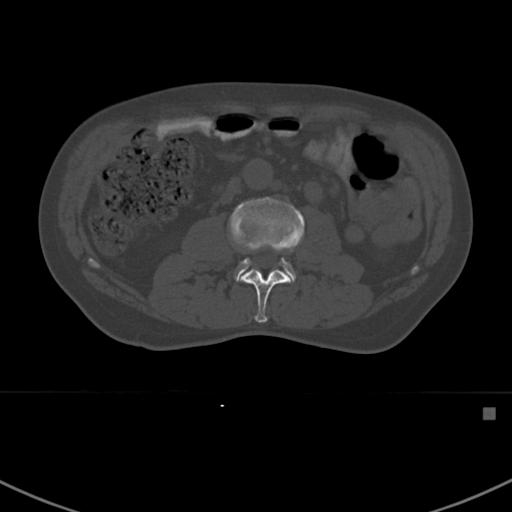
CT including the spine, one axial slice. Position 276 of 412 along the scan axis. Bone window (W 1800 / L 400 HU). 512 × 512 image matrix. Patient: male, 59 years. From the clinical record (not read from this slice): primary cancer: prostate.
Annotated regions visible in this slice (semi-automatically segmented with operator editing):
- L2 vertebra: bounding box [x1, y1, x2, y2] px = [240, 269, 291, 323]
- L3 vertebra: [228, 197, 305, 282]